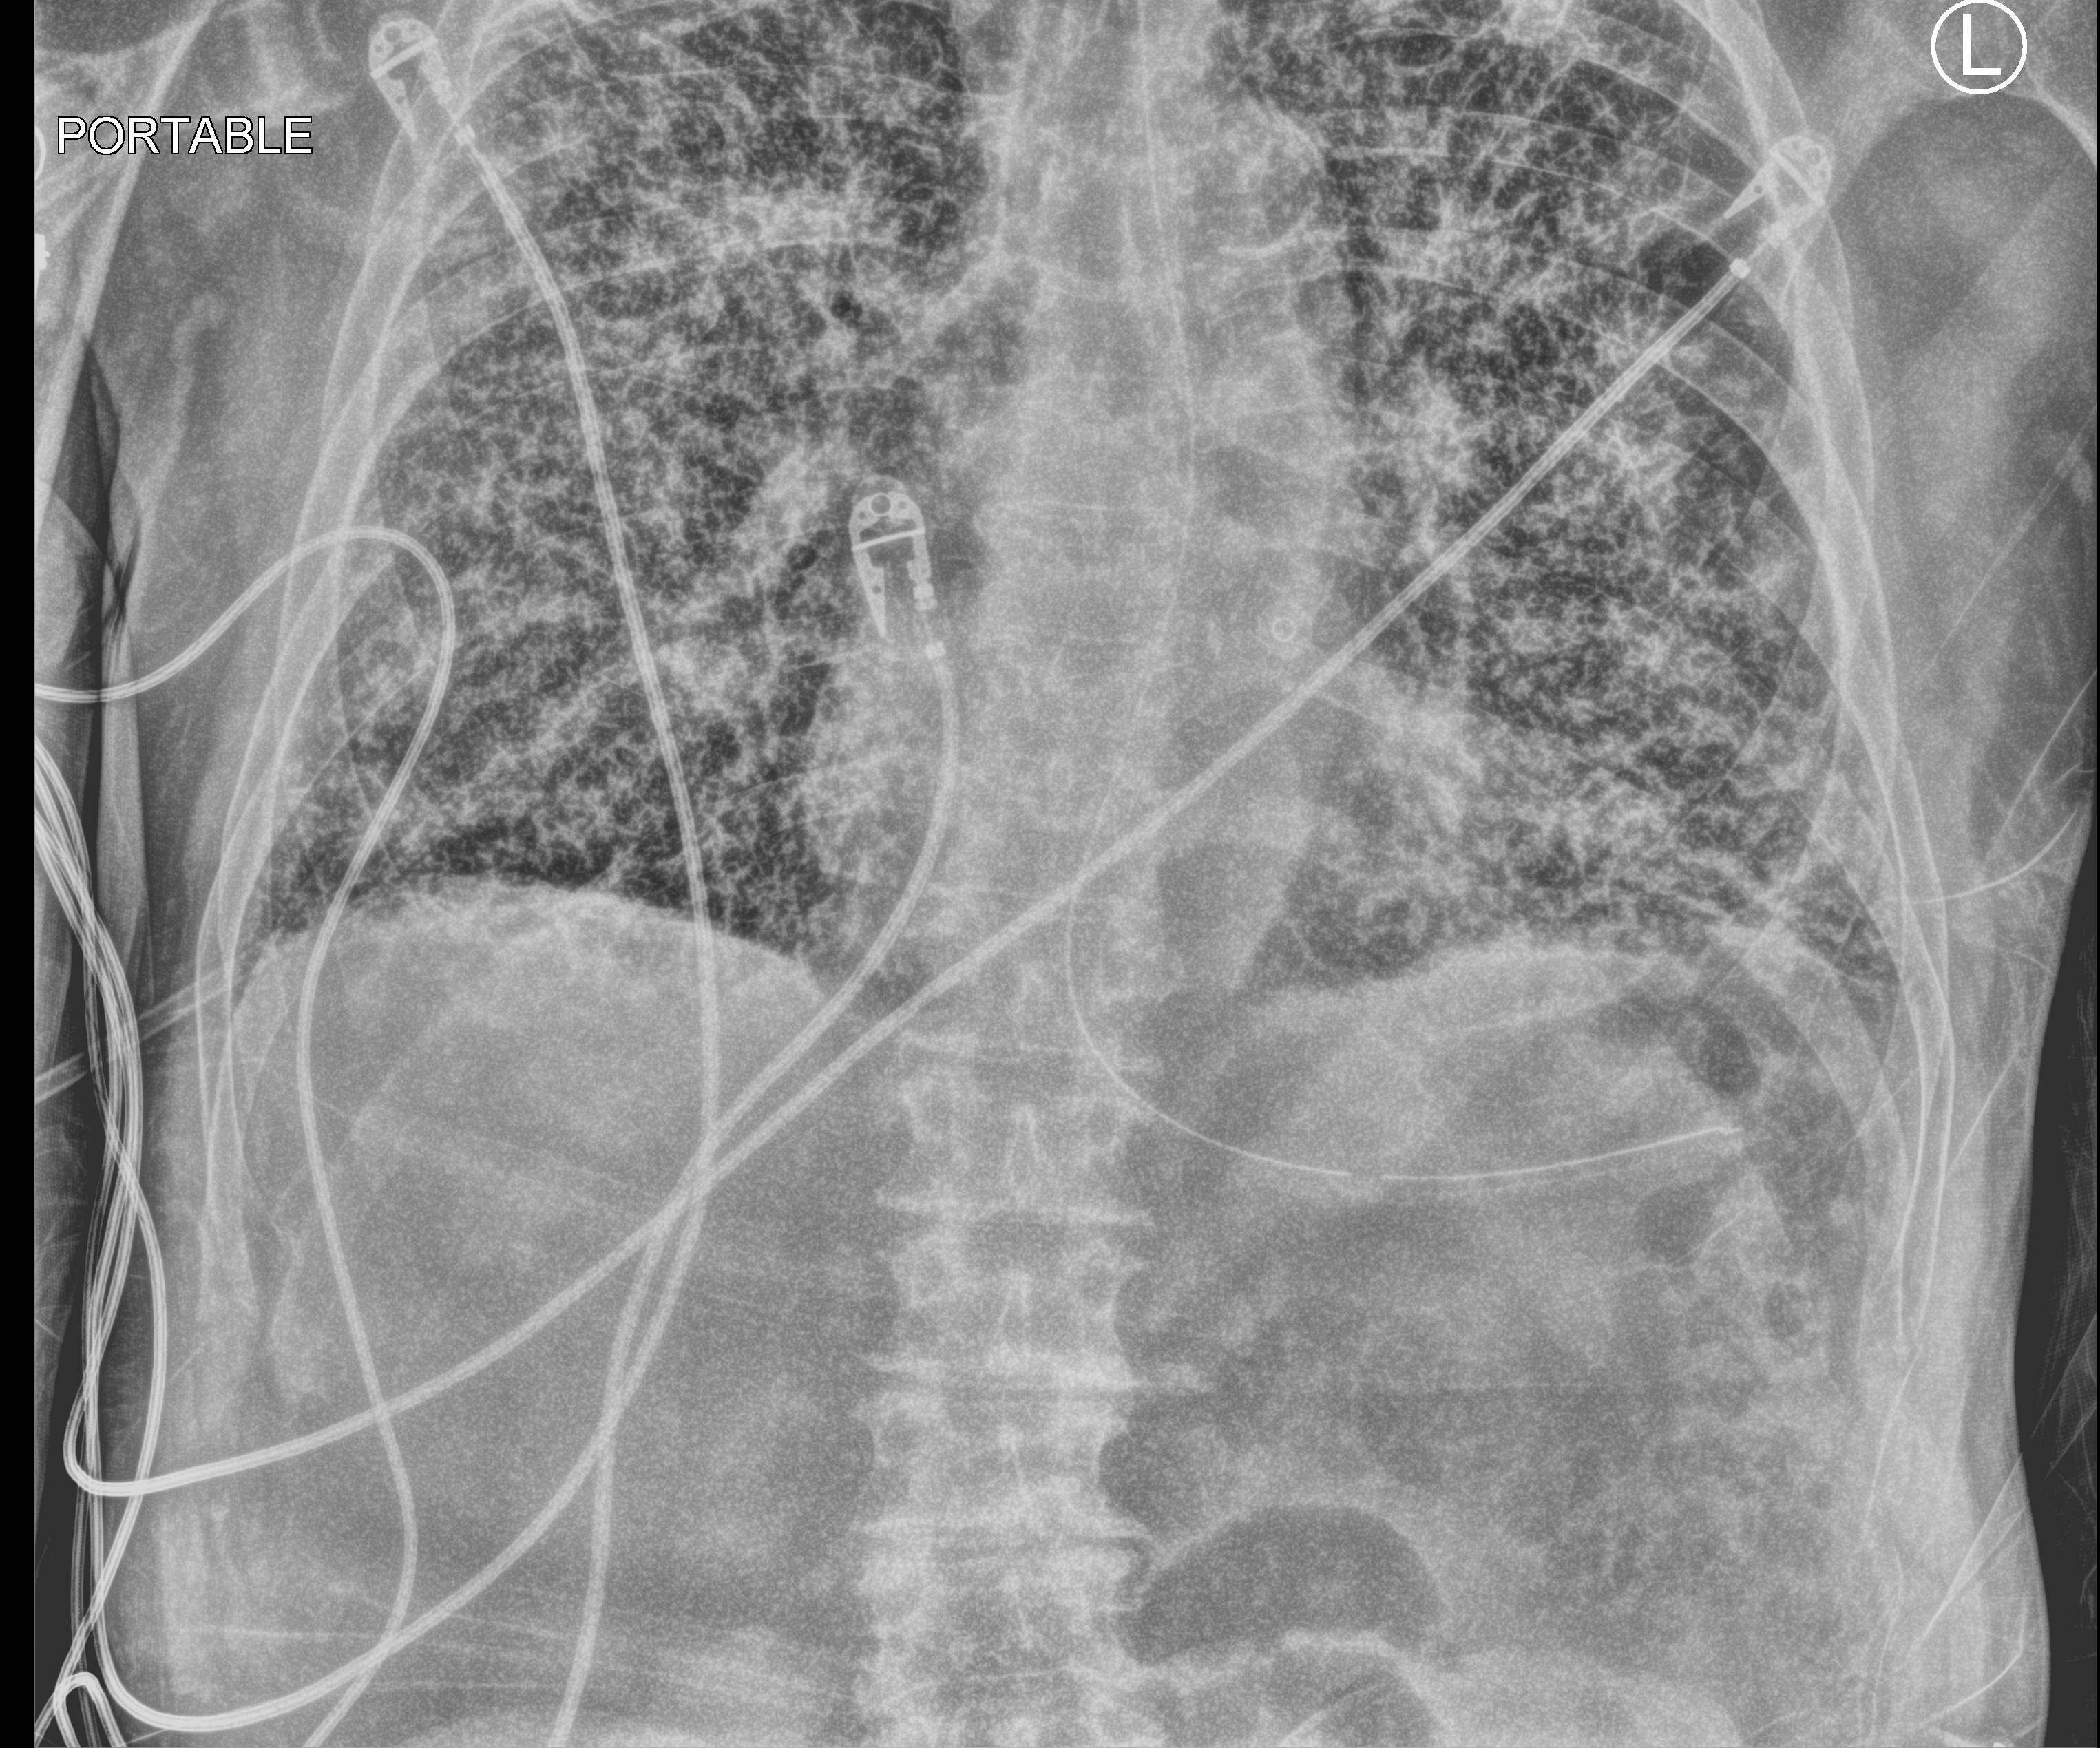
Chest X-ray (portable); anteroposterior (AP) projection. Patient hospitalised with COVID-19; male, aged 75–90 years.
From the hospital-stay record, not from the radiograph (when in the stay this image was taken is not recorded): mechanically ventilated during this hospital stay: yes.